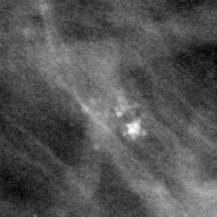
Cropped region of a digitized screen-film mammogram centred on a radiologist-marked abnormality; left breast; MLO view.
Finding: calcifications, morphology pleomorphic, distribution regional; BI-RADS assessment category 4; subtlety rating 4 on a 1 (subtle) to 5 (obvious) scale; pathology (as recorded): benign.